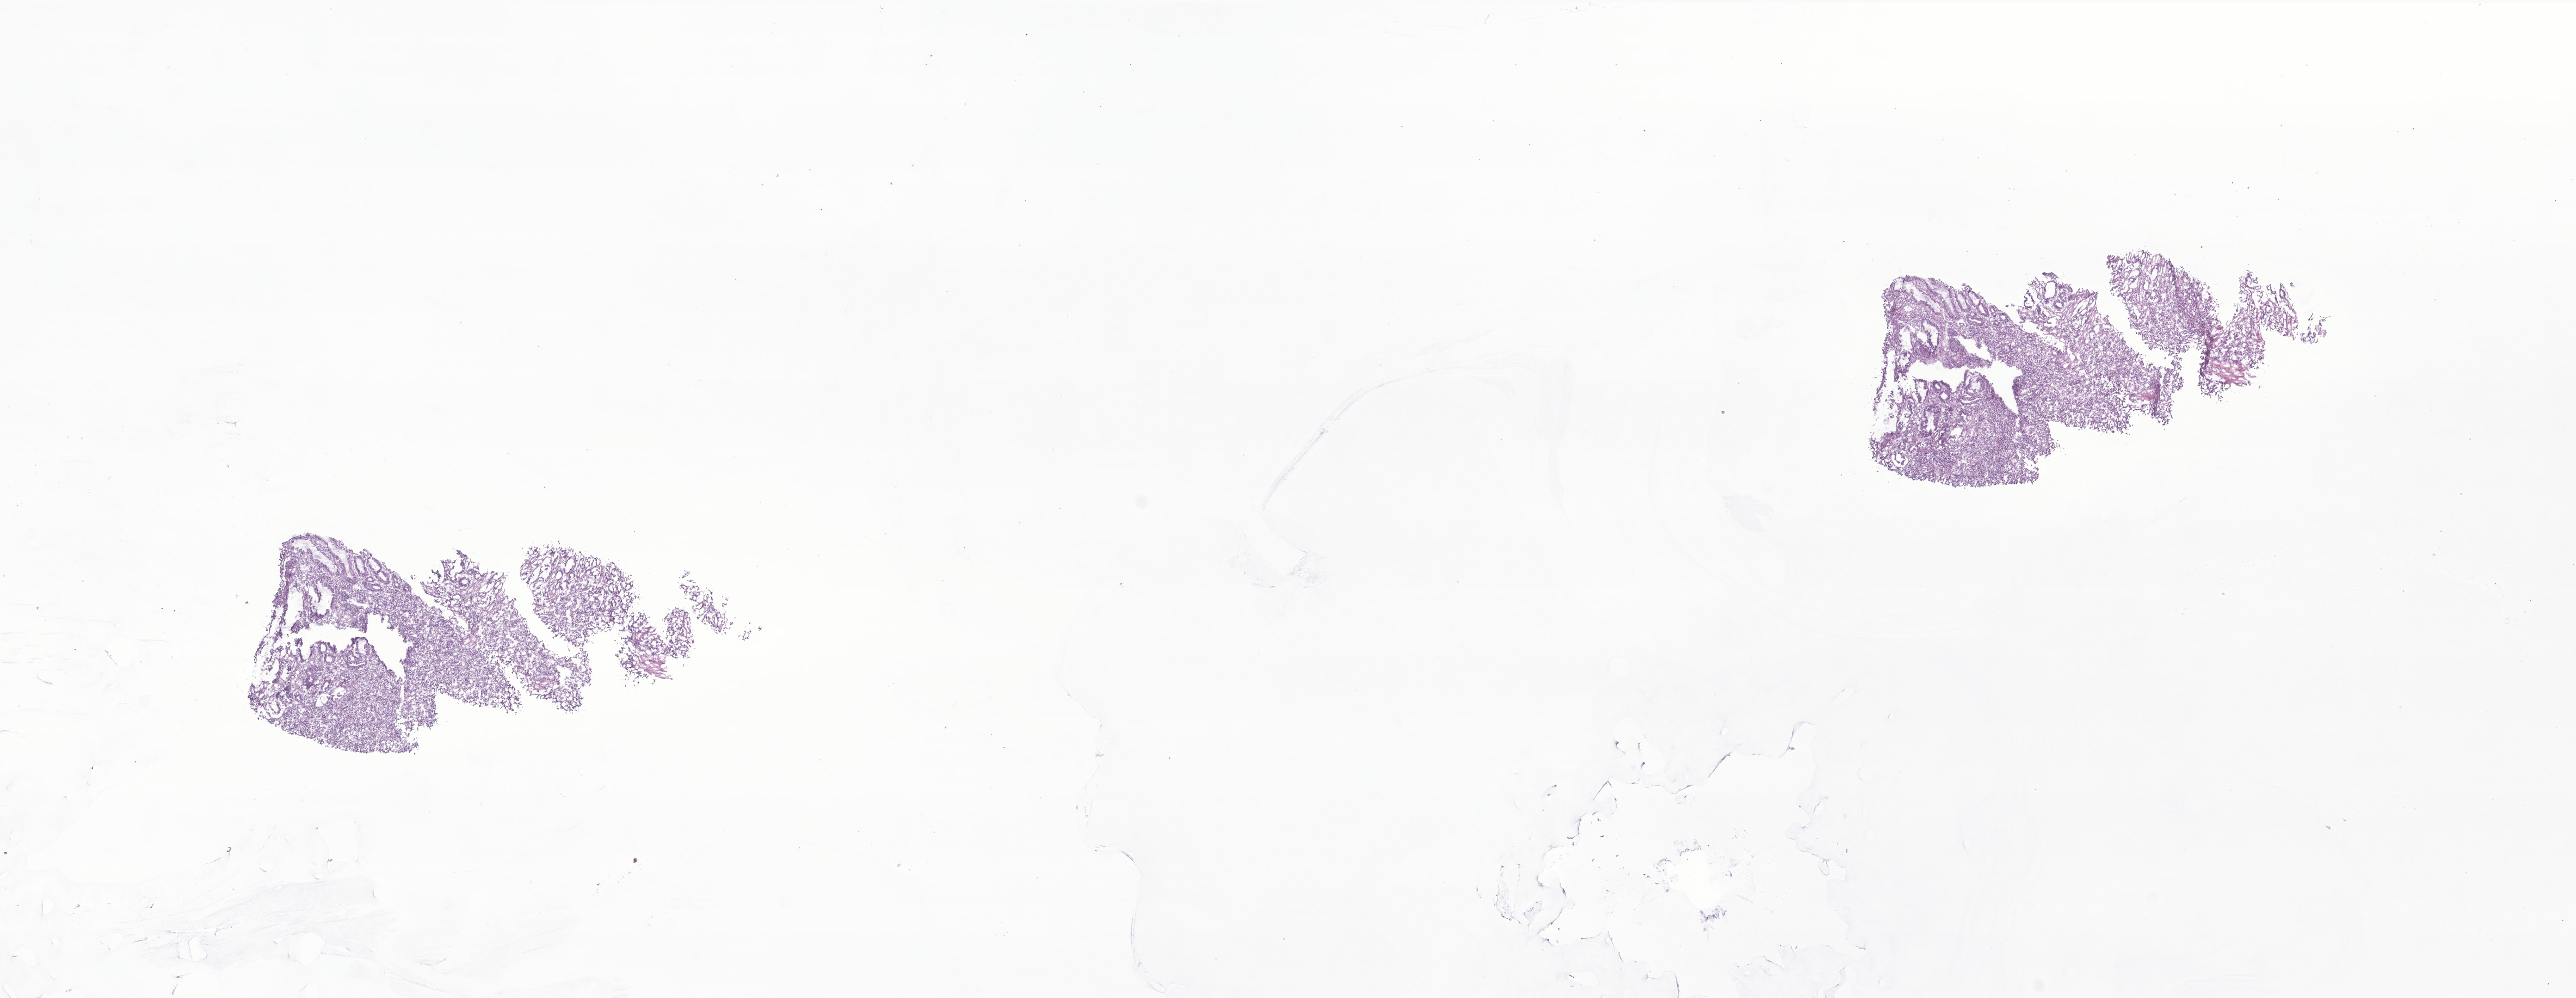
Digitized hematoxylin and eosin (H&E)-stained section of tumor tissue from the pyloric antrum, a low-resolution overview of the entire scanned area, about 20.0 x 7.7 mm. Frozen section (OCT-embedded). Patient: male, age 216 months (18 years).
* diagnosis: Gastrointestinal stromal tumor